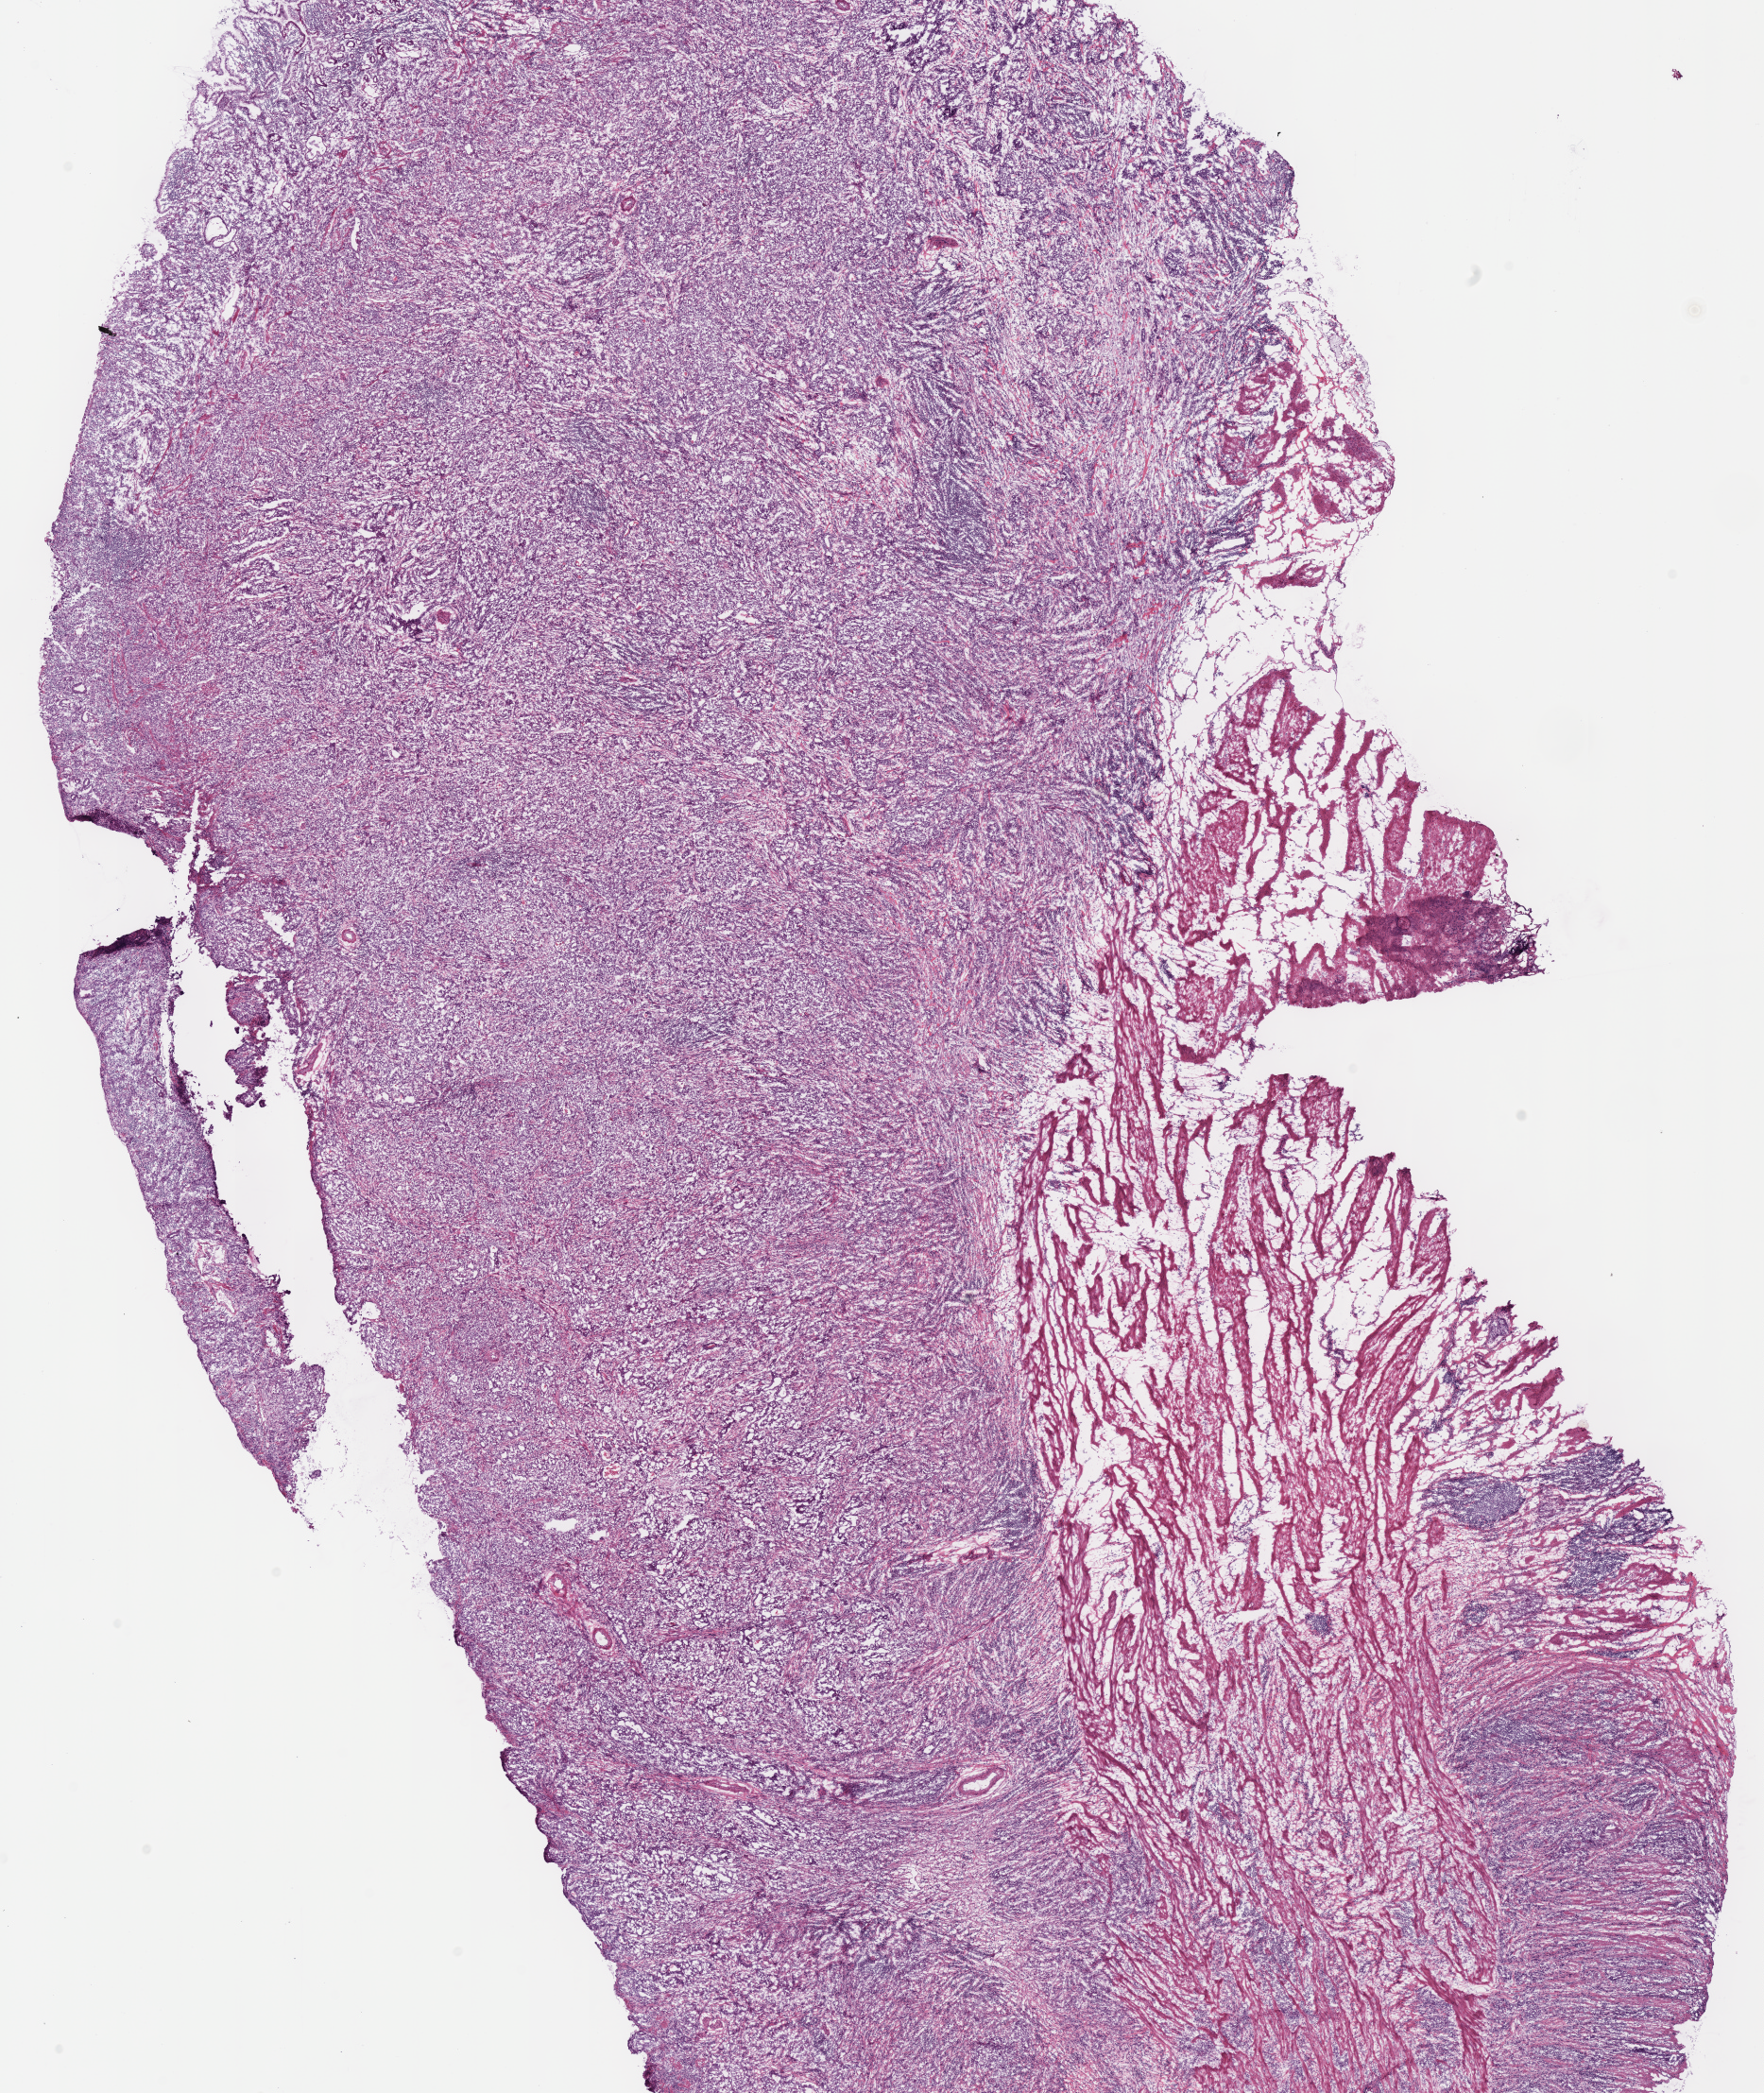
Digitized H&E tissue section (whole slide), low-resolution overview of the scanned area, about 14.7 x 17.4 mm (from a 40x scan); frozen section; stomach, primary tumour sample. Patient: female, age at initial diagnosis 62 years. Histologic grade: G2 (moderately differentiated). Composition of this section per pathologist review: tumour cells 80%, tumour nuclei 61%, normal cells 5%, stromal cells 15%, necrosis 0%. Infiltration values recorded for this section: lymphocyte infiltration 30%, monocyte infiltration 0%, neutrophil infiltration 0%.
AJCC pathologic stage: IIB. Diagnosis: Adenocarcinoma, NOS (body of stomach).